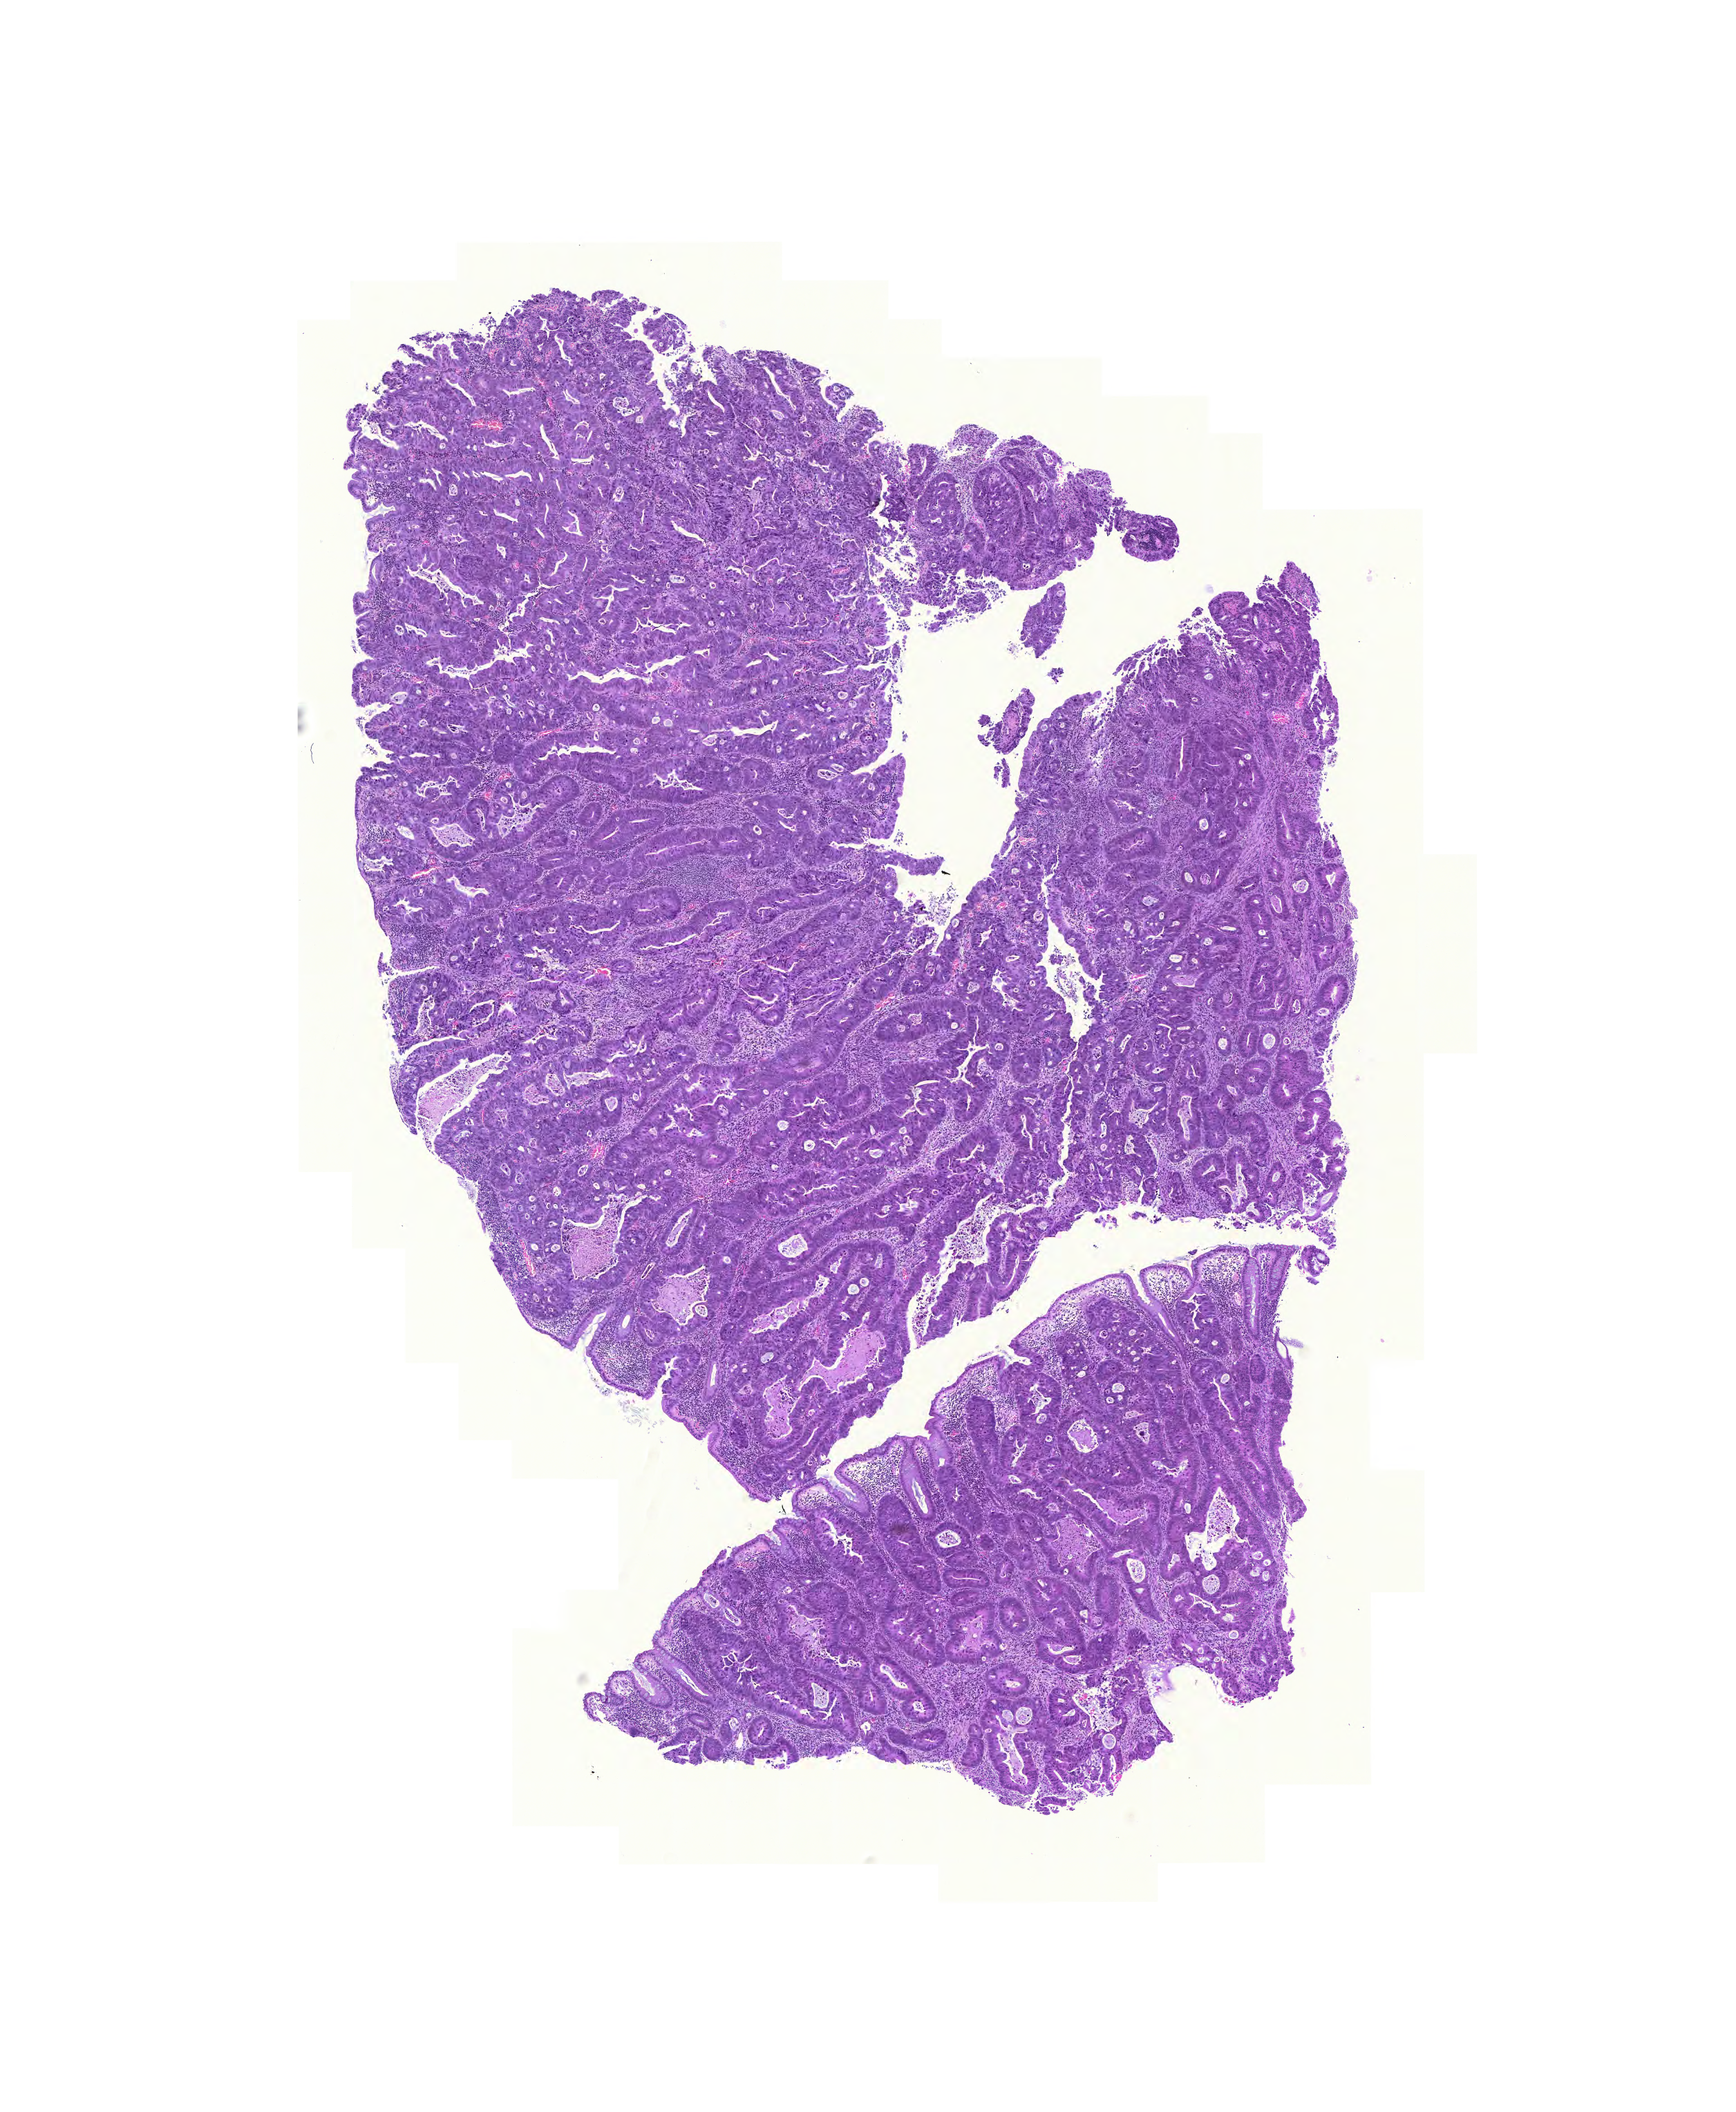
H&E-stained whole-slide image, low-resolution overview of the scanned area, about 9.3 x 11.4 mm; FFPE section; primary tumour sample from the colon. Male patient; age at initial diagnosis 63 years.
AJCC pathologic stage: IIA. Diagnosis: Adenocarcinoma, NOS. Lymph nodes positive (case pathology): 0 of 35 examined.